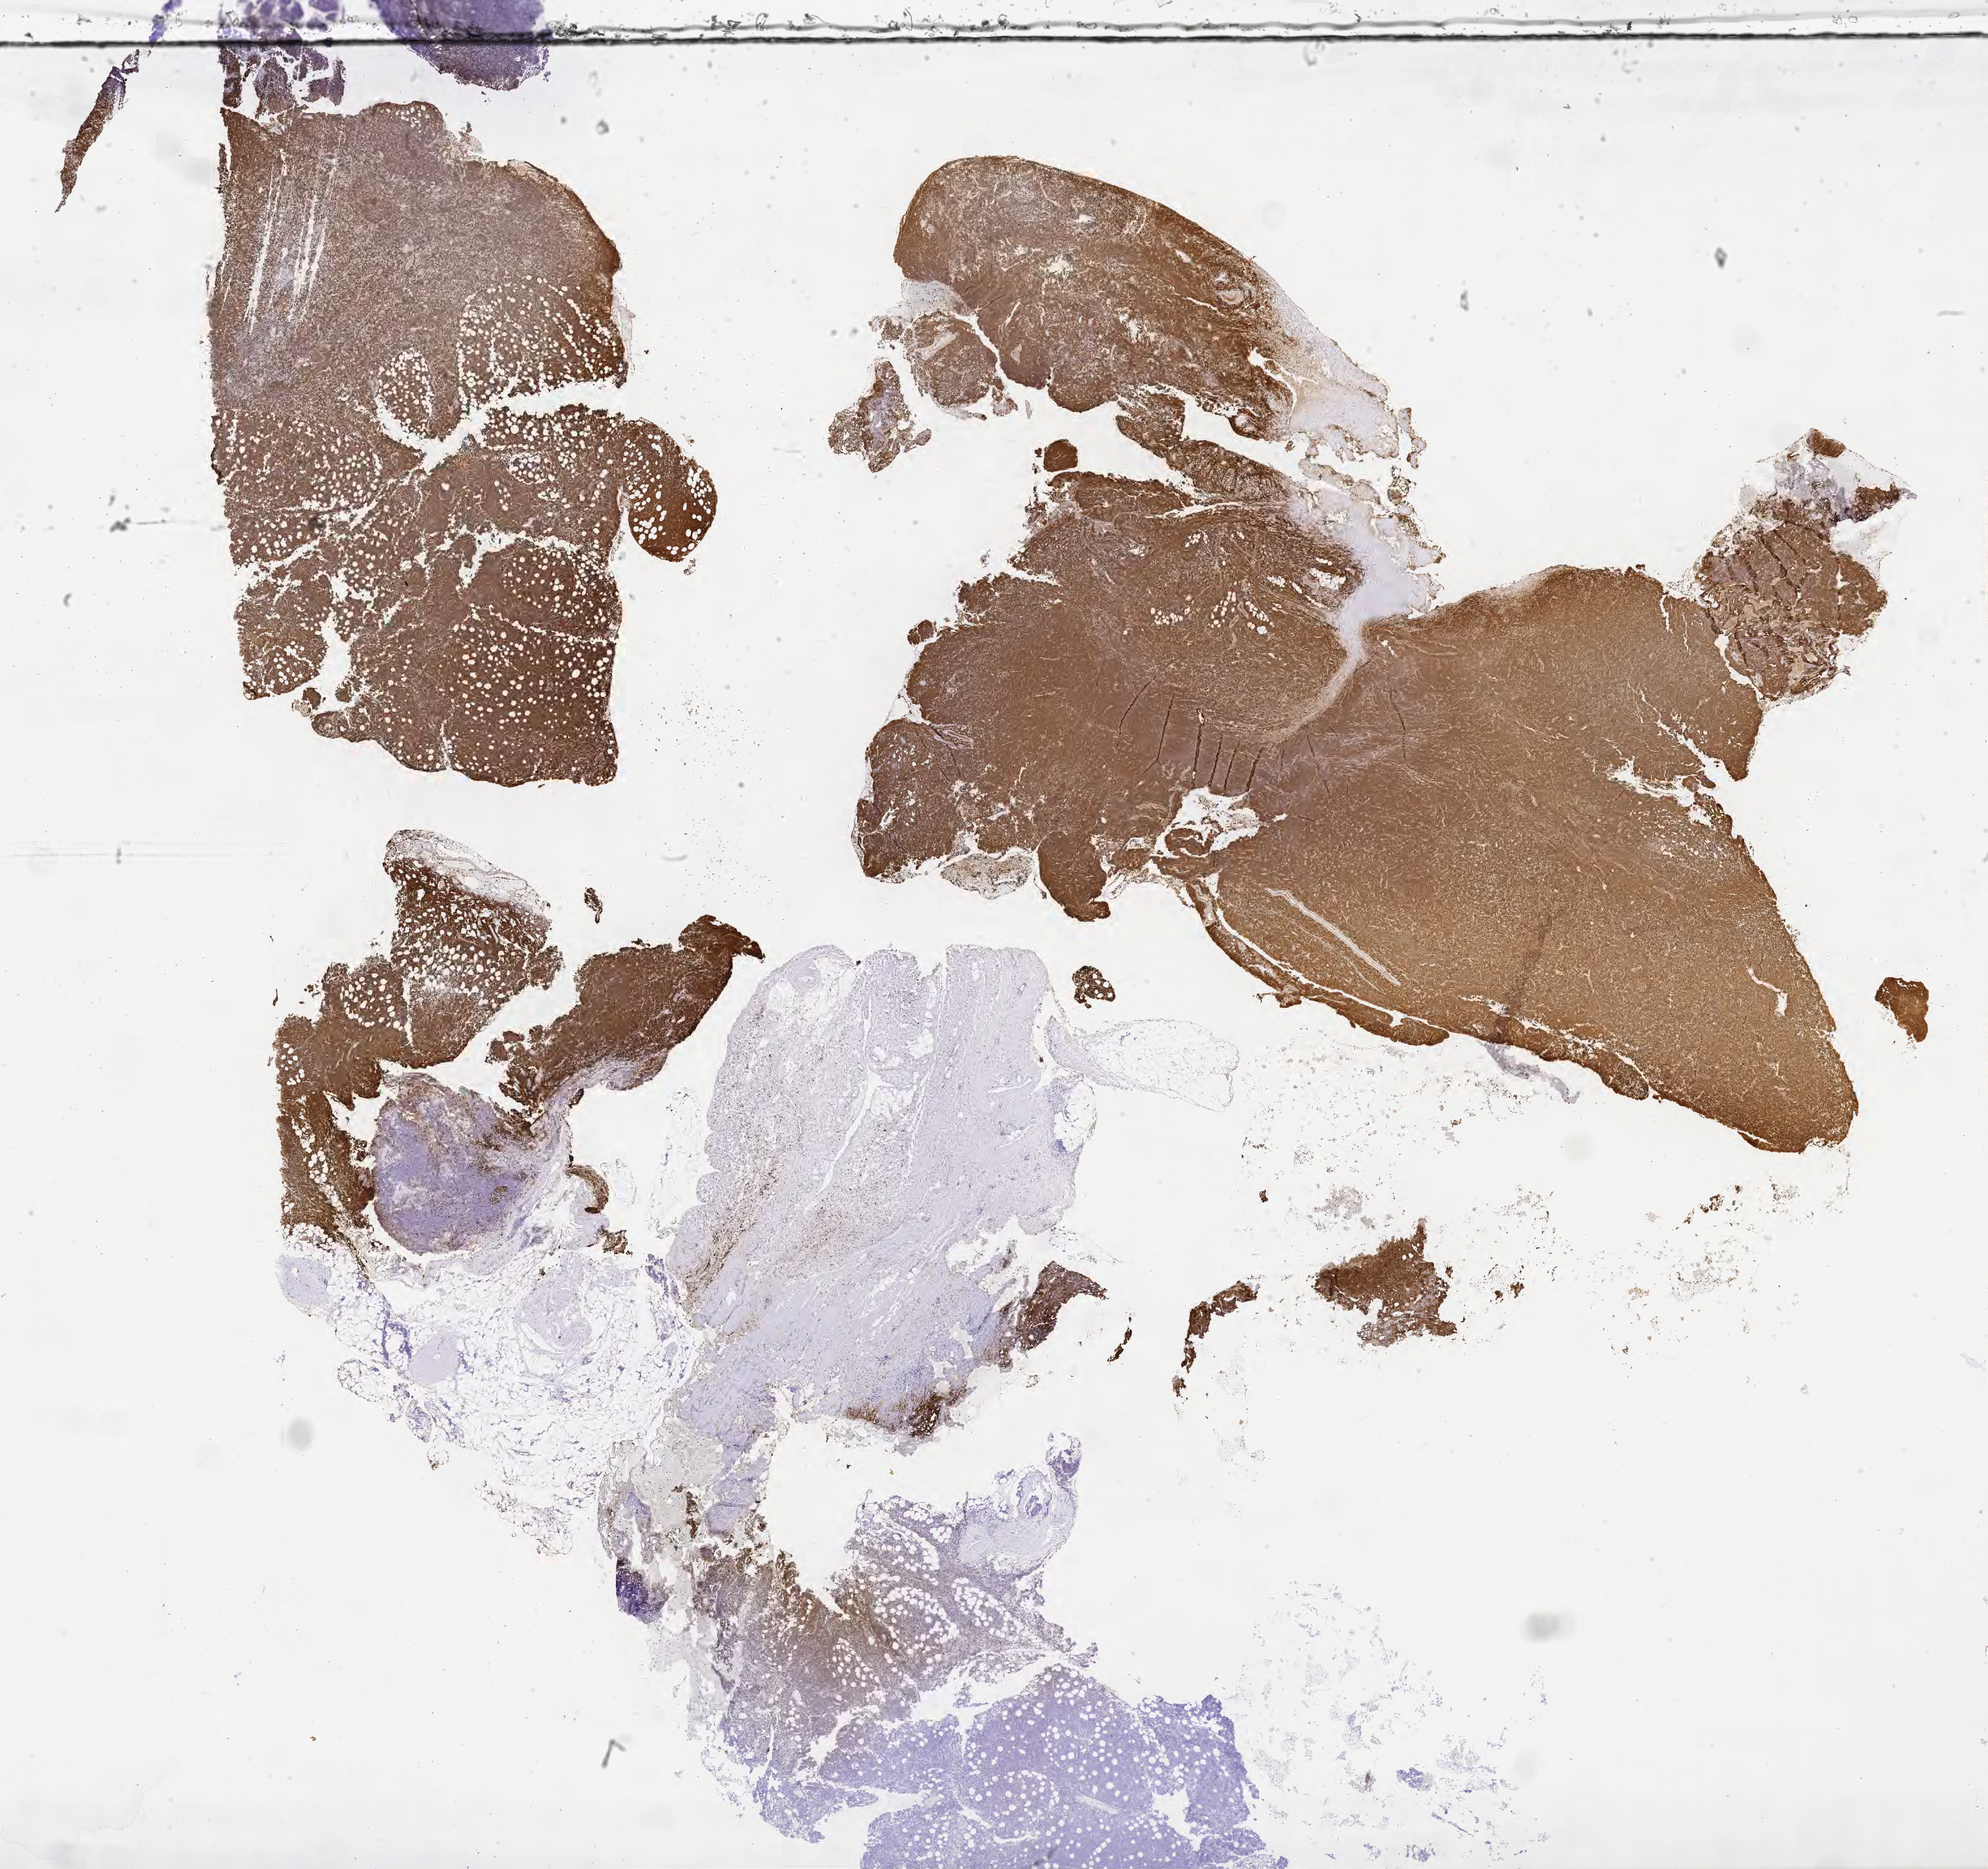
Whole-slide image, immunohistochemical stain for Ki-67 — a low-resolution overview of the entire scanned area, about 24.7 x 23.2 mm, specimen: tumor tissue. Patient: female, aged 72.
- histologic diagnosis: Burkitt lymphoma, NOS